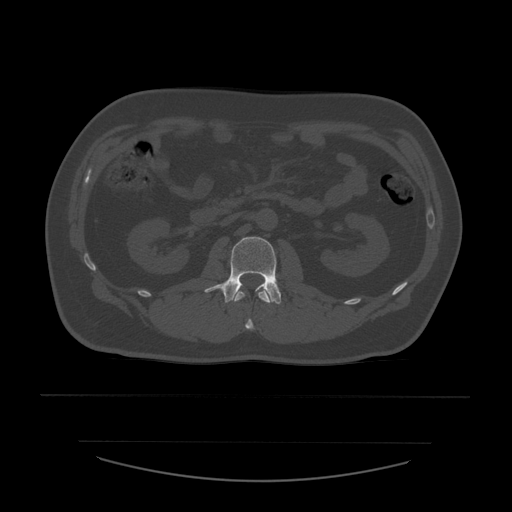
CT including the spine, one axial slice. Position 207 of 532 along the scan axis. Reconstruction kernel STANDARD. 120 kVp. Bone window (W 1800 / L 400 HU). 1.25 mm slice thickness. 512 × 512 image matrix. Patient age 44 years. From the clinical record (not read from this slice): primary cancer: soft tissue sarcoma.
Outlined on this slice (semi-automatically segmented with operator editing):
- L1 vertebra: bounding box <233,290,273,331> (left, top, right, bottom; pixels)
- L2 vertebra: <205,237,282,305>